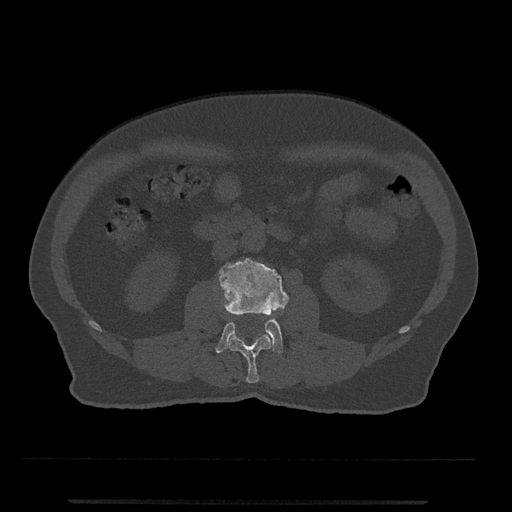
CT including the spine, one axial slice. Slice 232 of 797 in the series (ordered by position). Reconstruction kernel Br40s/3. Bone window (W 1800 / L 400 HU). 0.5 mm slice thickness. 512 × 512 image matrix. Male patient, age 63 years. From the clinical record (not read from this slice): primary cancer: prostate.
Outlined on this slice (semi-automatic segmentation, software-assisted and operator-edited):
- L2 vertebra: bounding box (x1, y1, x2, y2) in pixels: (228, 333, 272, 383)
- L3 vertebra: (215, 257, 289, 354)